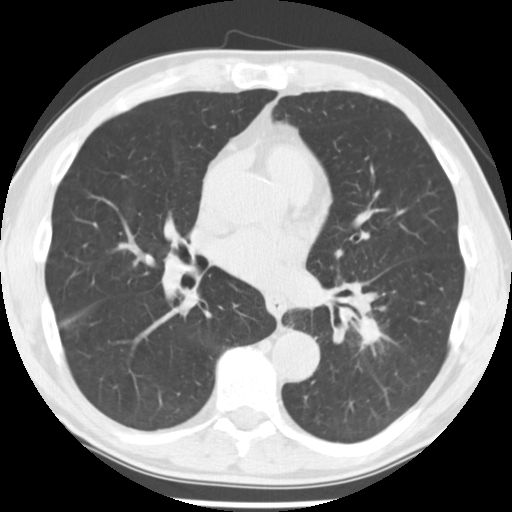
Low-dose screening chest CT, axial slice. Third screening round (two years after baseline). Lung window (W 1500 / L -600 HU). 2.5 mm slice thickness. Standard (soft-tissue) reconstruction kernel (STANDARD). 120 kVp. Slice 116 of 242 in the series. Male, age 64 years at enrolment.
Lesion marked by an expert reader, bounding box <351,317,390,350> (left, top, right, bottom; pixels). No non-calcified nodule or mass ≥4 mm was recorded by the screening reader at this exam. Participant outcome: lung cancer diagnosed 203 days after this screen — adenocarcinoma, NOS, left lower lobe, stage IV (AJCC 6th edition), 44 mm at pathology.